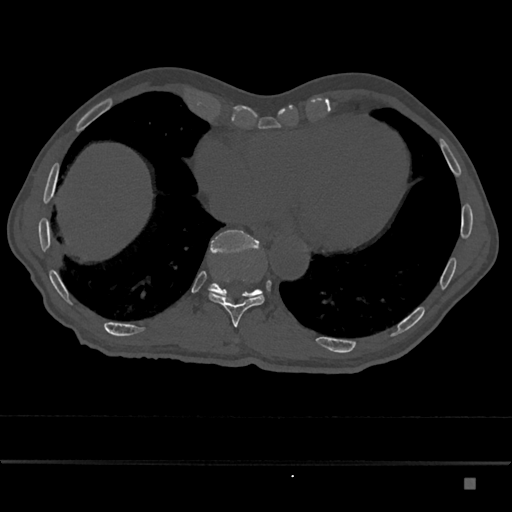
CT including the spine, one axial slice; position 724 of 797 along the scan axis; reconstruction kernel Br40s/3; 120 kVp; bone window (W 1800 / L 400 HU); 0.5 mm slice thickness; 512 × 512 image matrix. Patient: male, 72 years. Case-level facts recorded for this patient, not image findings: primary cancer: prostate.
Outlined on this slice (semi-automatically segmented with operator editing):
- T10 vertebra: bounding box (x1, y1, x2, y2) in pixels: (209, 292, 265, 328)
- T11 vertebra: (208, 230, 263, 298)